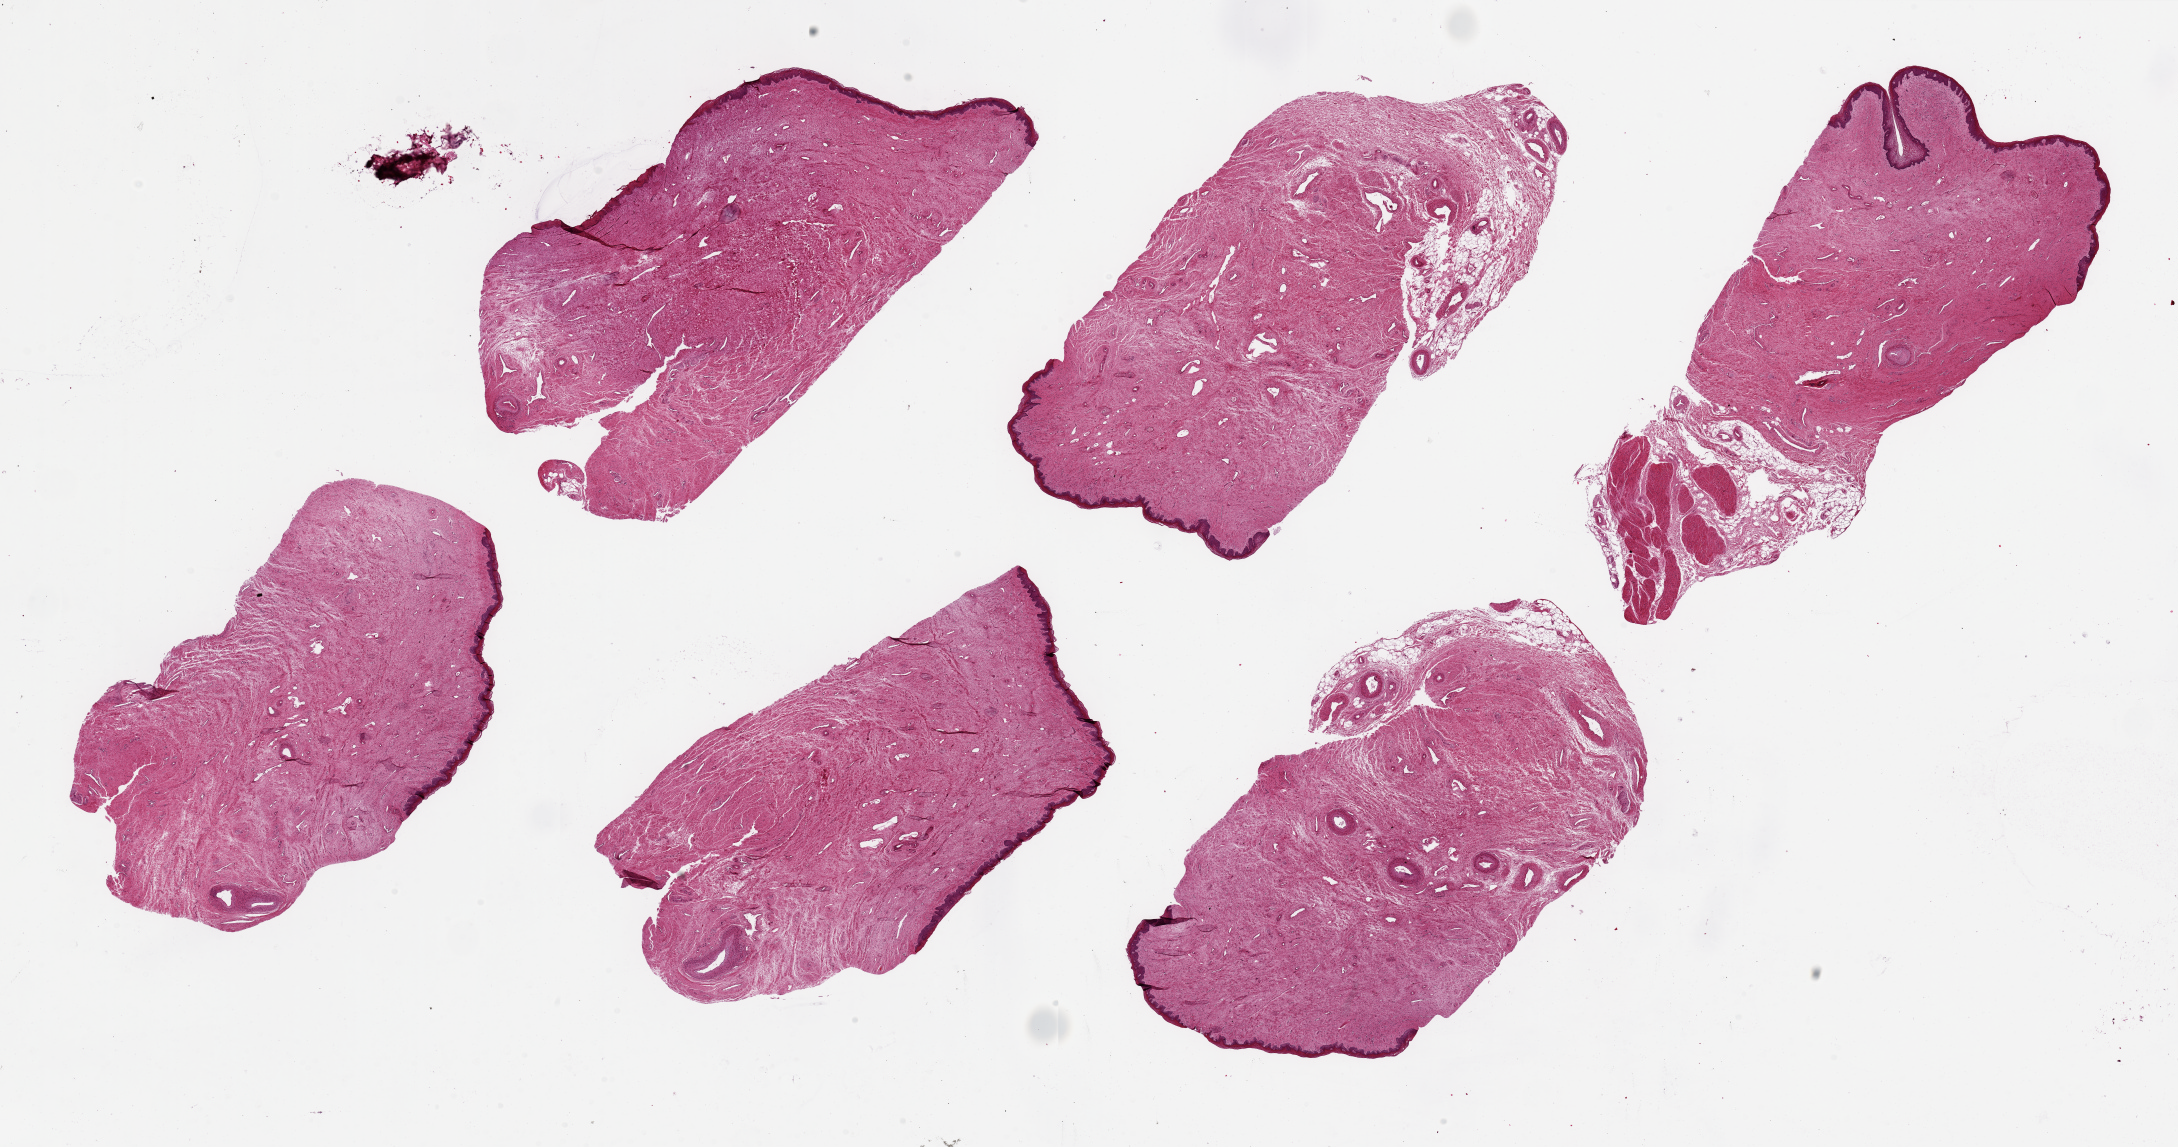
Digitized haematoxylin and eosin-stained section, a low-resolution overview of the entire scanned area, about 34.5 x 18.1 mm. PAXgene-fixed, paraffin-embedded tissue. Sampled site (target tissue): vagina. Tissue donor sample. Female donor.
Pathologist's review note for this sample: 6 pieces up to 10x4 mm.